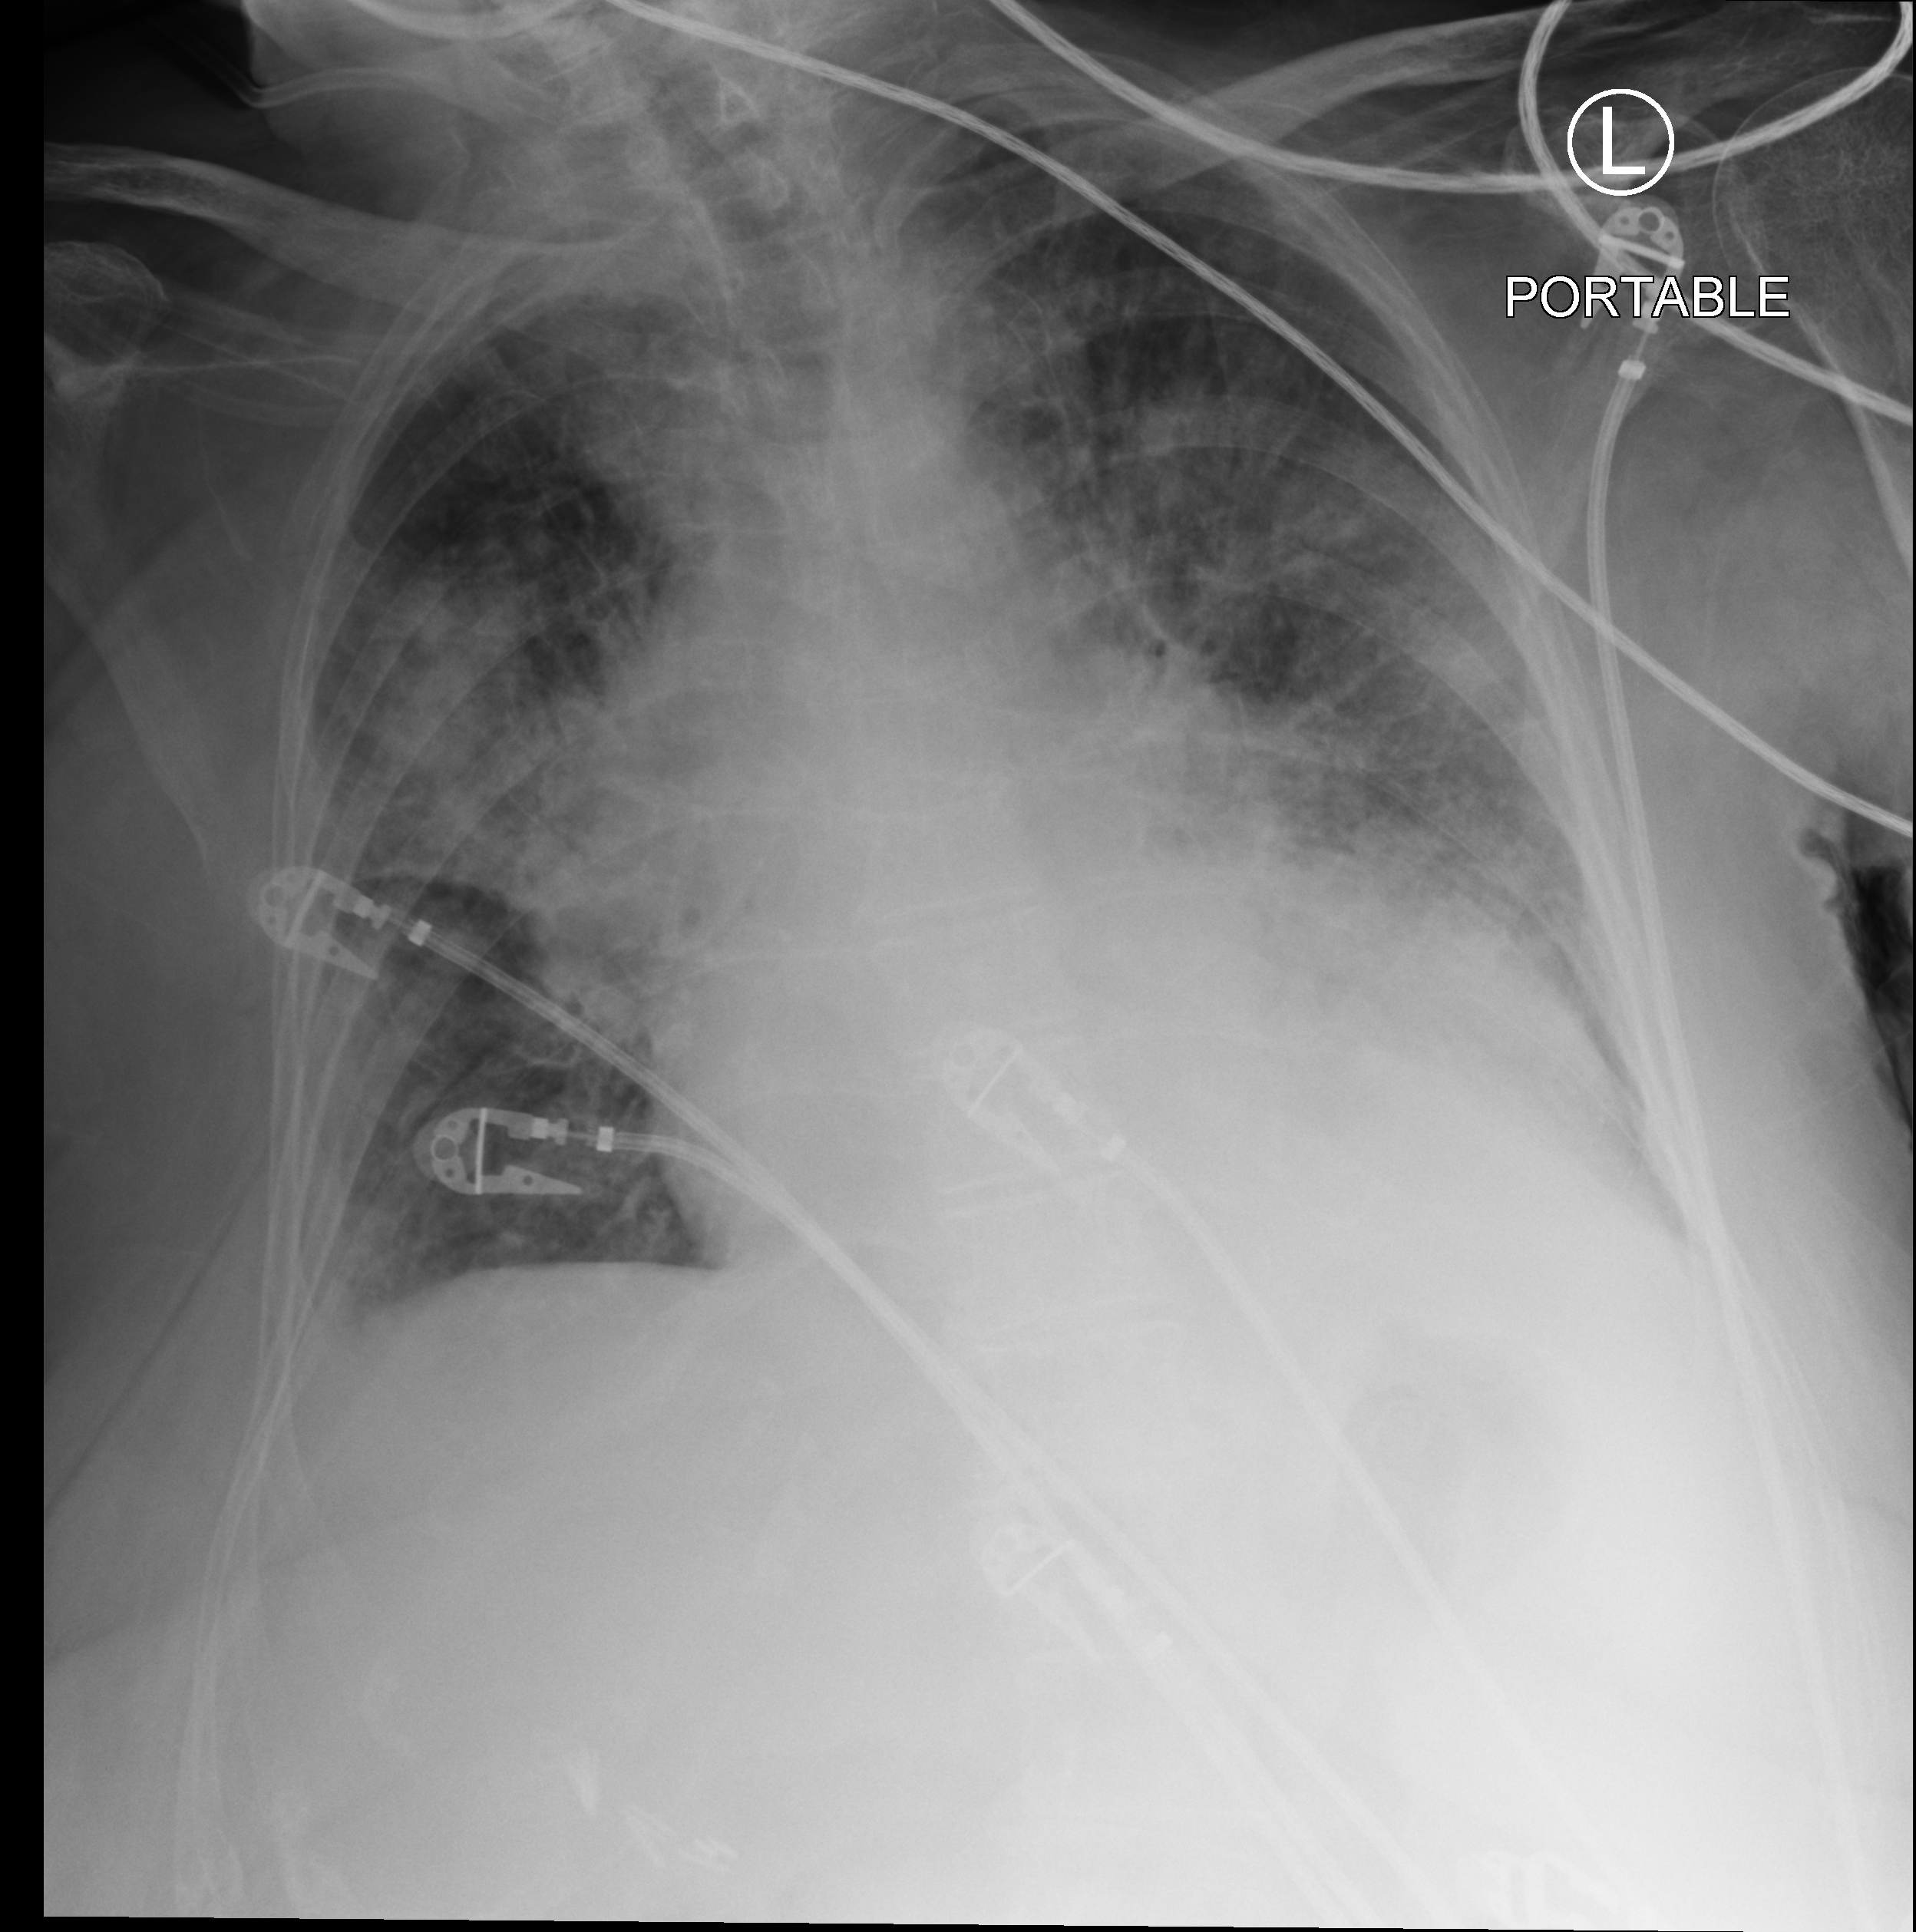
Bedside chest radiograph (computed radiography); anteroposterior (AP) projection. Patient hospitalised with COVID-19; female, aged 75–90 years.
Admission-level facts for this patient (not findings on this image; timing relative to this image not recorded): mechanically ventilated during this hospital stay: no; length of hospital stay: 4 days; COPD (admission record): no.